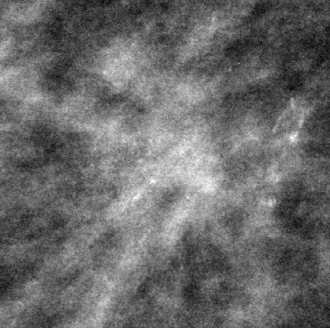
Crop from a digitized film mammogram around one marked abnormality, right breast, MLO view.
- Marked abnormality: mass, shape architectural distortion, margins ill defined; BI-RADS assessment category 5; subtlety rating 4 on a 1 (subtle) to 5 (obvious) scale; pathology result (as recorded, not read from the image): malignant.